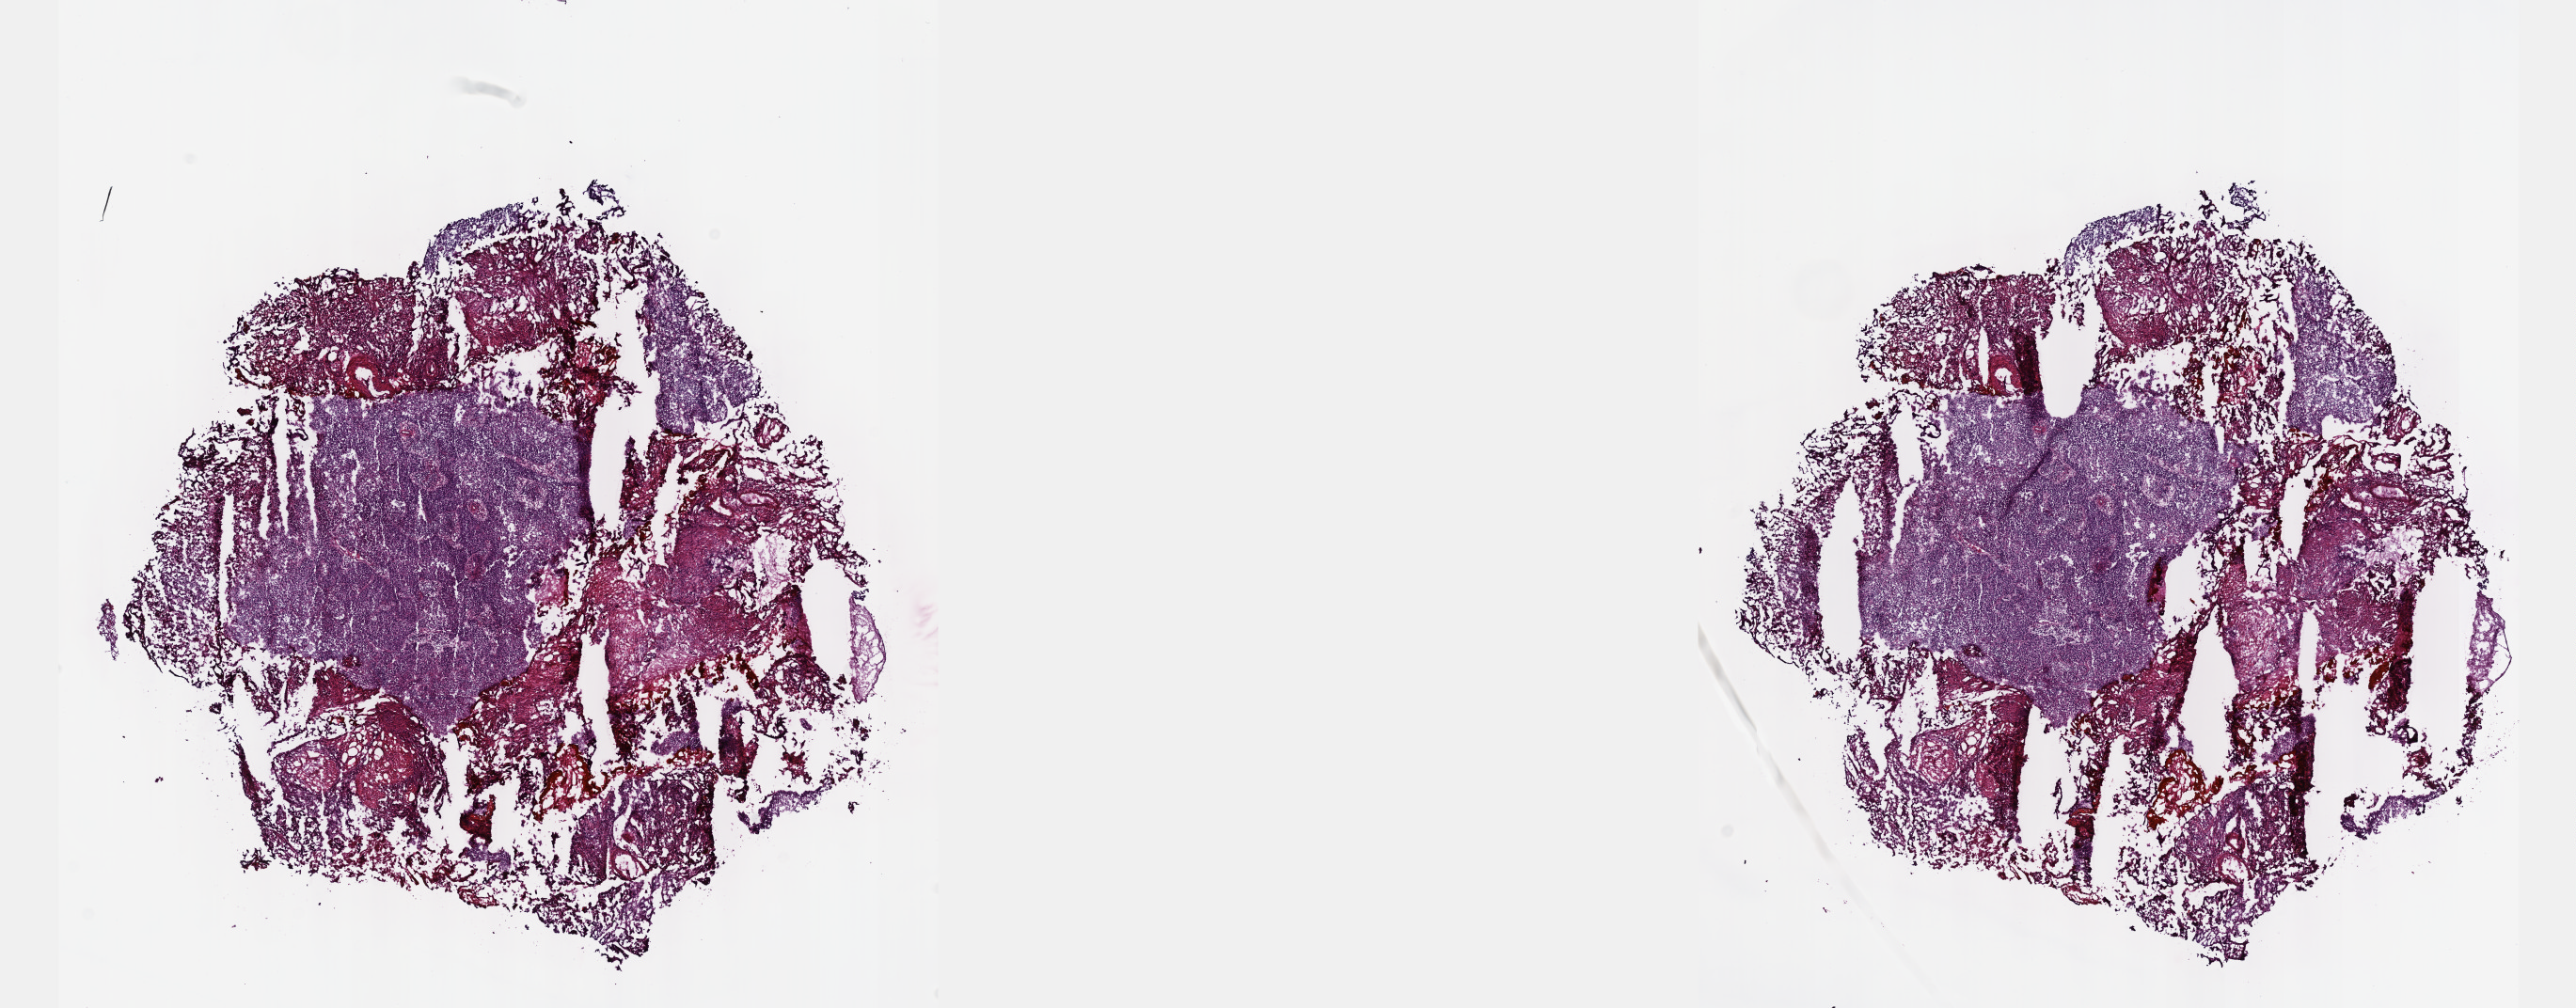
Whole-slide histology image, Hematoxylin and eosin (H&E) stained — shown as a low-resolution overview of the whole scanned area (about 22.1 x 8.7 mm). Frozen section from the top of the tissue portion. Bladder, primary tumour sample. Patient: female, age at initial diagnosis 76 years. Histologic grade: high grade. Composition of this section per pathologist review: tumour cells 80%, tumour nuclei 75%, normal cells 20%, stromal cells 0%, necrosis 0%. Infiltration values recorded for this section: lymphocyte infiltration 3%, monocyte infiltration 0%, neutrophil infiltration 0%.
AJCC pathologic stage: II (7th edition). TNM: NX M0. Pathologic diagnosis: Transitional cell carcinoma.